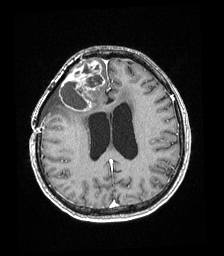
Brain MRI from a brain-tumour surgery series, one axial slice; position 78 of 192 along the scan axis; T1-weighted post-contrast; 224 × 256 image matrix, field of view 219 × 250 mm. From the clinical record (not read from this slice): histopathology: Astrocytoma; WHO grade: 4; IDH mutation: yes; tumour location: Right superficial frontal.
Outlined on this slice (expert manual segmentation):
- tumour: bounding box <59,61,105,112> (left, top, right, bottom; pixels)